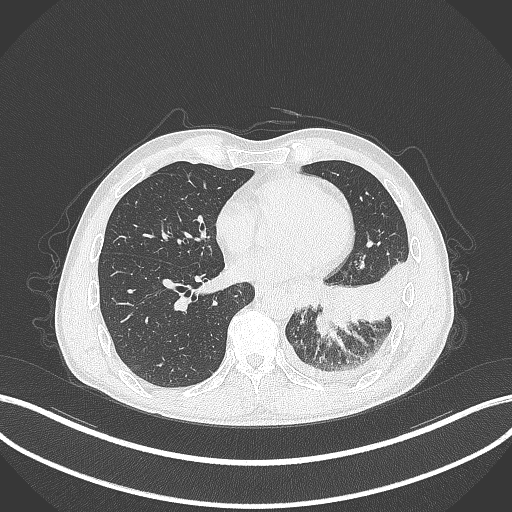
Chest CT, one axial slice. Position 117 of 295 along the scan axis. Reconstruction kernel B70f. 120 kVp. Lung window (W 1500 / L -600 HU). 512 × 512 image matrix. Male patient, age 47 years. From the clinical record (not read from this slice): clinical TNM (as recorded): T3 N1 M1c; histopathological grade: G3.
Structures marked on this image (bounding box drawn by a radiologist):
- lung tumour (recorded histology: small cell carcinoma): bounding box [x1, y1, x2, y2] px = [311, 307, 336, 339]